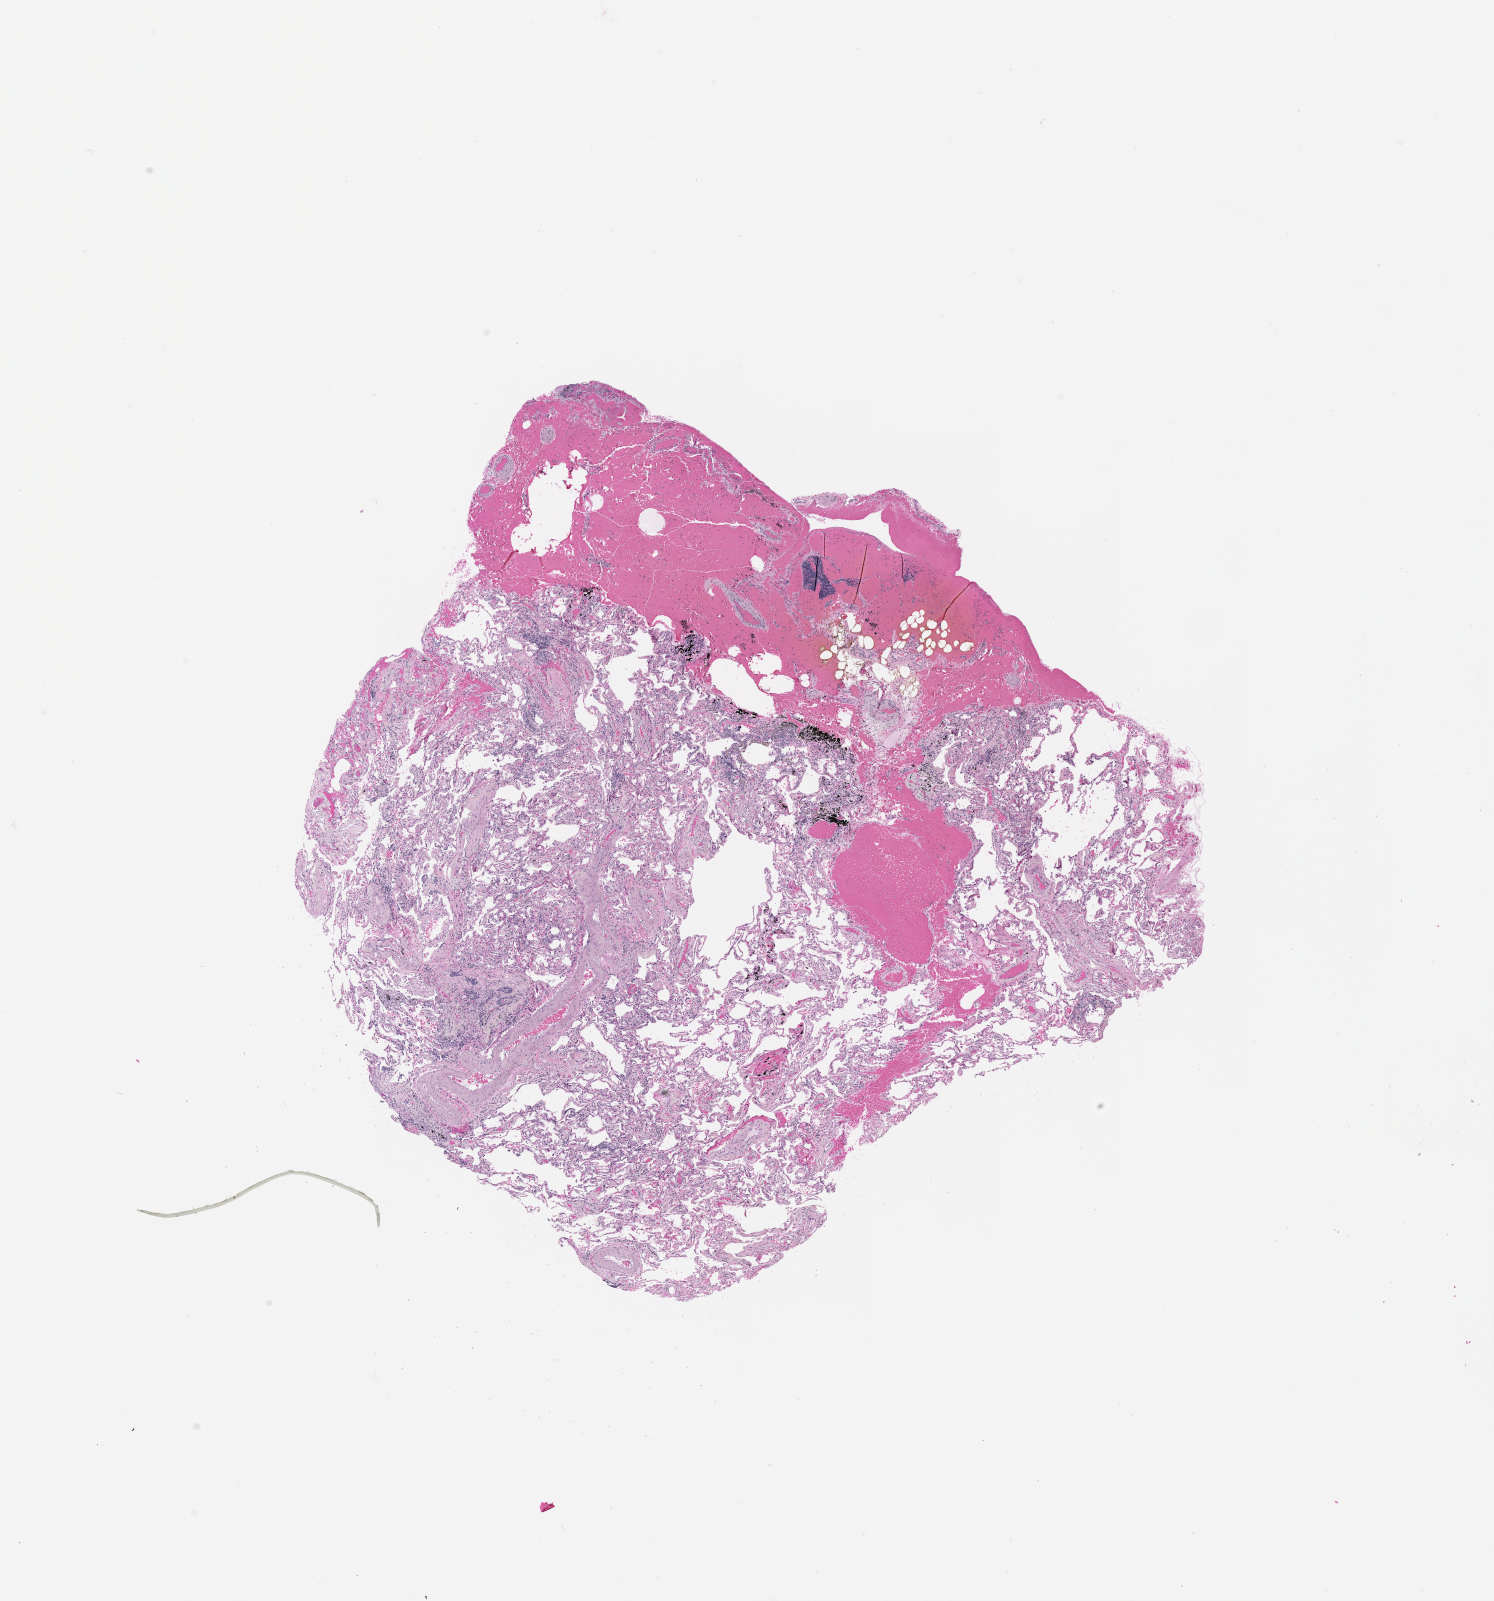
Whole-slide histology image, Hematoxylin and eosin (H&E) stained — a low-resolution overview of the entire scanned area, about 12.0 x 12.9 mm (acquisition: 20x scan), lung, normal (non-tumour) tissue. Patient sex: female.
• this section: normal (non-tumour) tissue from the same patient
• patient diagnosis (cohort enrolment): squamous cell carcinoma (lung)